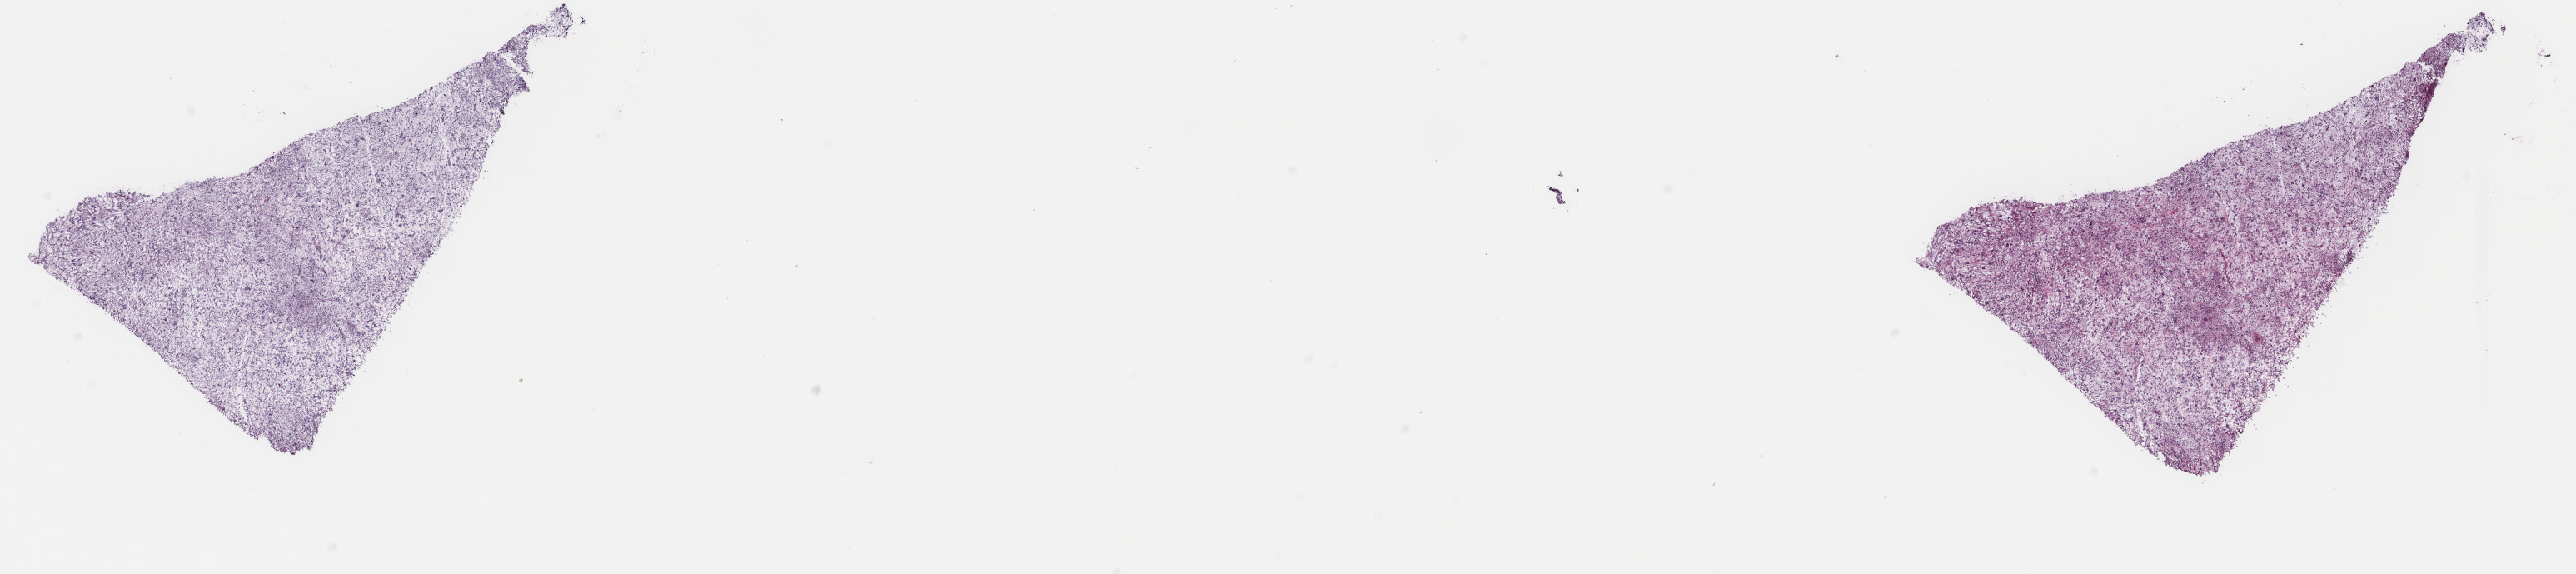
H&E whole-slide image — low-resolution overview of the scanned area, about 24.6 x 5.5 mm, frozen section from the top of the tissue portion, sample: primary tumour, retroperitoneum and peritoneum. Male patient; age at initial diagnosis 59 years. Composition of this section per pathologist review: tumour cells 85%, tumour nuclei 95%, normal cells 0%, stromal cells 0%, necrosis 5%. Inflammatory infiltration, as recorded: lymphocyte infiltration 3%, monocyte infiltration 0%, neutrophil infiltration 0%.
* pathologic diagnosis: Dedifferentiated liposarcoma (retroperitoneum)